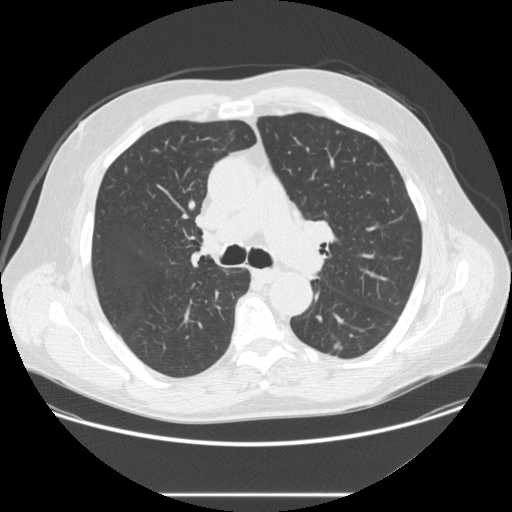
Low-dose screening chest CT, one axial slice. Slice 163 of 262 in the series (ordered by position). Reconstruction kernel STANDARD. 120 kVp. Lung window (W 1500 / L -600 HU). 2.5 mm slice thickness. 512 × 512 image matrix, field of view 420 × 420 mm.
Outlined on this slice (manually delineated by an expert):
- lesion 1 (tumor, lower lobe of left lung): bounding box <335,343,342,349> (left, top, right, bottom; pixels)